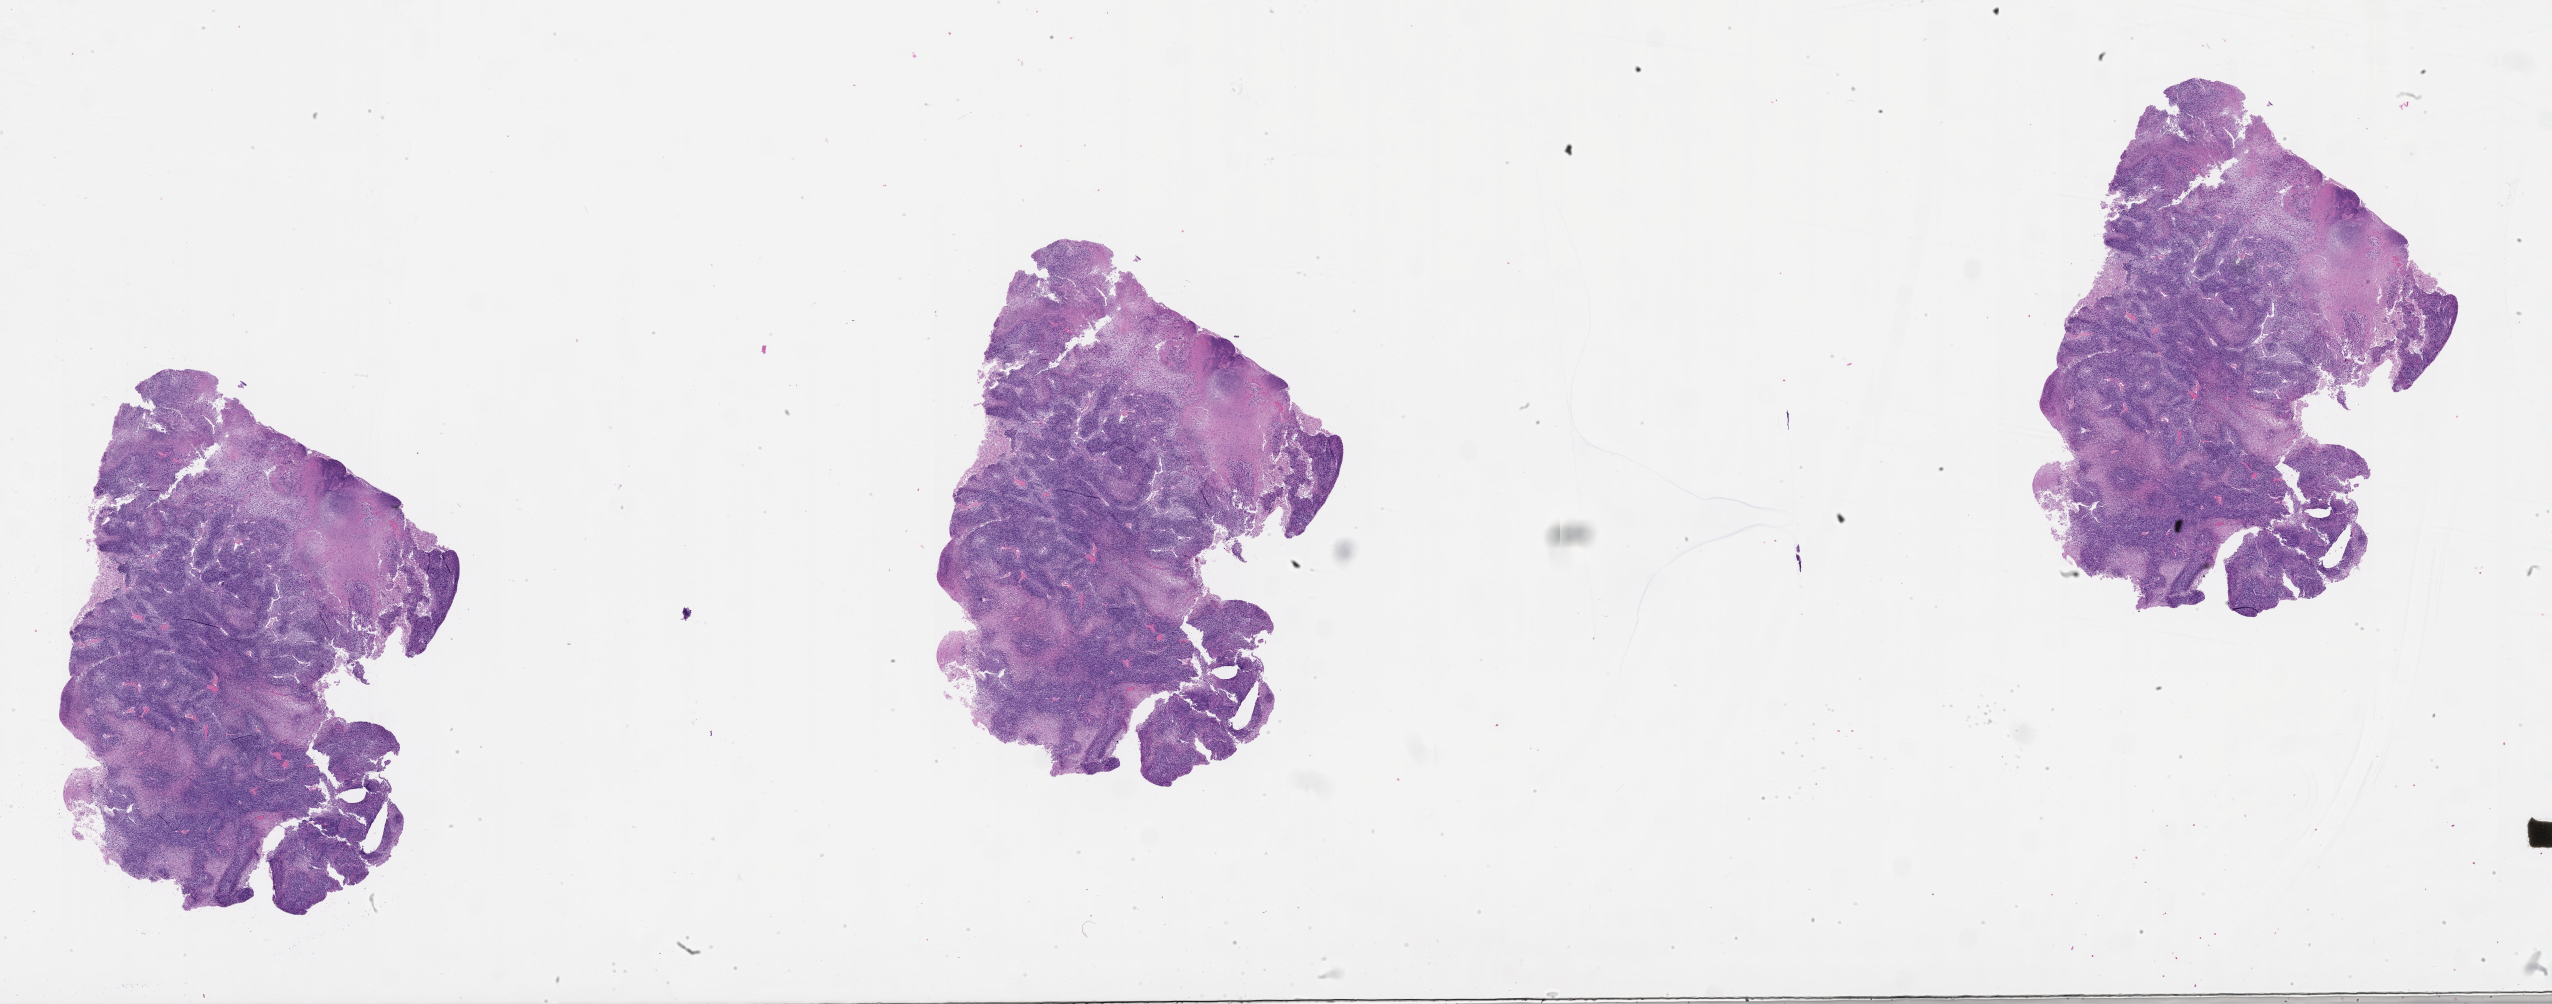
H&E whole-slide image — a low-resolution overview of the entire scanned area, about 41.1 x 16.2 mm.
- patient diagnosis (cohort enrolment): sarcoma (site not recorded at cohort level)